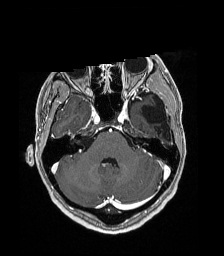
Brain MRI from a brain-tumour surgery series, one axial slice; position 130 of 192 along the scan axis; T1-weighted post-contrast; 1 mm slice thickness; 224 × 256 image matrix, field of view 224 × 256 mm. From the clinical record (not read from this slice): histopathology: Low grade glioma; IDH mutation: no; tumour location: Left Parieto-Occipital Intraventricular.
Structures marked on this image (outlined manually by an expert reader):
- previous resection cavity: box from (x=142, y=98) to (x=170, y=138) px